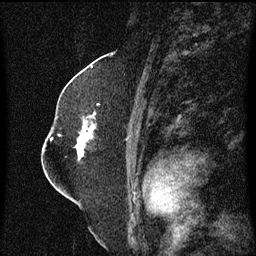
Breast MRI (dynamic contrast-enhanced), one sagittal slice. Dynamic contrast-enhanced series, image 2 of 3 at this slice position (ordered by acquisition). 1.5 T. TE 4.2 ms, TR 8.4 ms. 256 × 256 image matrix, field of view 200 × 200 mm. Female patient, age 52 years. From the clinical record (not read from this slice): setting: breast cancer imaged before/during neoadjuvant chemotherapy; receptor status: HR-positive, HER2-negative.
Outlined on this slice (semi-automatically segmented with operator editing):
- analysis volume of interest (the breast-tissue region the enhancement analysis was run in; not a lesion): bounding box [x1, y1, x2, y2] px = [76, 104, 101, 161]
- tumour enhancement mask (voxels above the 70 % enhancement threshold inside the analysis volume of interest): [77, 114, 97, 159]